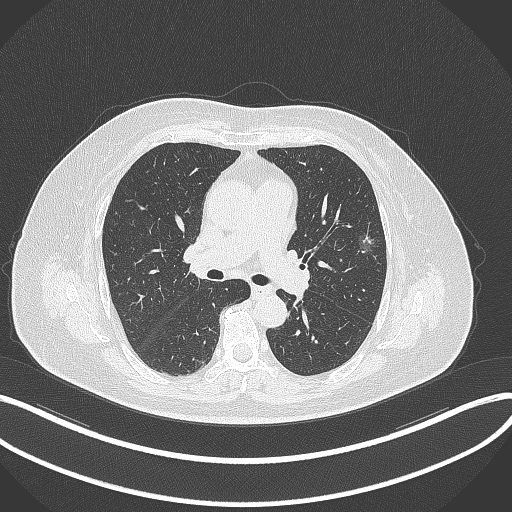
Chest CT, one axial slice. Slice 214 of 315 in the series (ordered by position). Lung window (W 1500 / L -600 HU). 1 mm slice thickness. 512 × 512 image matrix. Patient: female, 76 years. Case-level facts recorded for this patient, not image findings: clinical TNM (as recorded): T1b N0 M0; histopathological grade: G1-2.
Annotated regions visible in this slice (bounding box drawn by a radiologist):
- lung tumour (recorded histology: adenocarcinoma): bounding box [x1, y1, x2, y2] px = [355, 230, 378, 258]